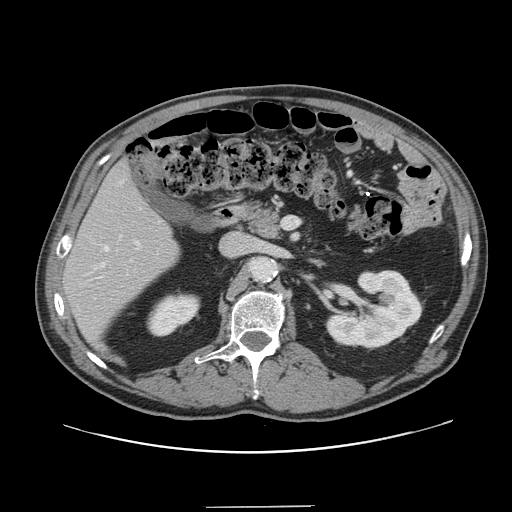
Contrast-enhanced abdominal CT, one axial slice; slice 72 of 139 in the series (ordered by position); intravenous contrast given; soft-tissue window (W 400 / L 40 HU); 2.5 mm slice thickness; 512 × 512 image matrix, field of view 397 × 397 mm. Male patient, age 64 years. From the clinical record (not read from this slice): diagnosis: colorectal cancer liver metastases, imaged before liver resection; multiple liver metastases: yes; largest metastasis: 3.5 cm.
Outlined on this slice (expert manual segmentation):
- hepatic veins: box from (x=101, y=182) to (x=132, y=267) px
- liver: (x=64, y=164)–(x=179, y=345)
- planned liver remnant (the part of the liver to remain after resection): (x=64, y=165)–(x=179, y=344)
- portal vein (with intrahepatic branches): (x=99, y=241)–(x=140, y=278)